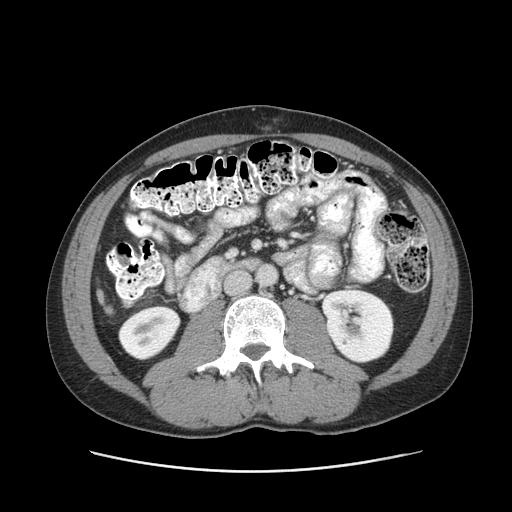
Contrast-enhanced abdominal CT (liver protocol), one axial slice; slice 22 of 93 in the series (ordered by position); 120 kVp; soft-tissue window (W 400 / L 40 HU); 2.5 mm slice thickness; 512 × 512 image matrix, field of view 380 × 380 mm. From the clinical record (not read from this slice): diagnosis: hepatocellular carcinoma (patient treated with transarterial chemoembolisation; whether this scan precedes or follows treatment is not stated here); TNM stage (as recorded): Stage-II; Child-Pugh class: A; tumour size: 1 cm.
Outlined on this slice (semi-automatically segmented with operator editing):
- liver parenchyma outside the tumour (the mass and vessels are separate outlines, so this box may not span the whole liver): bounding box [x1, y1, x2, y2] px = [96, 289, 104, 302]